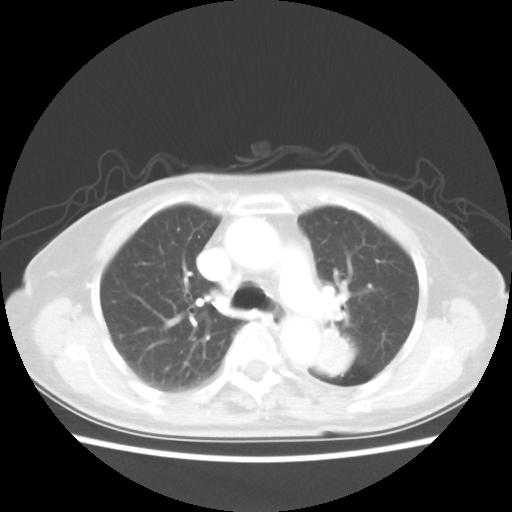
Chest CT, one axial slice. Position 33 of 50 along the scan axis. 80 kVp. Lung window (W 1500 / L -600 HU). 5 mm slice thickness. 512 × 512 image matrix. Patient: female, 81 years. From the clinical record (not read from this slice): clinical TNM (as recorded): T2 N0 M1a.
Structures marked on this image (bounding box drawn by a radiologist):
- lung tumour (recorded histology: squamous cell carcinoma): bounding box [x1, y1, x2, y2] px = [314, 323, 357, 377]